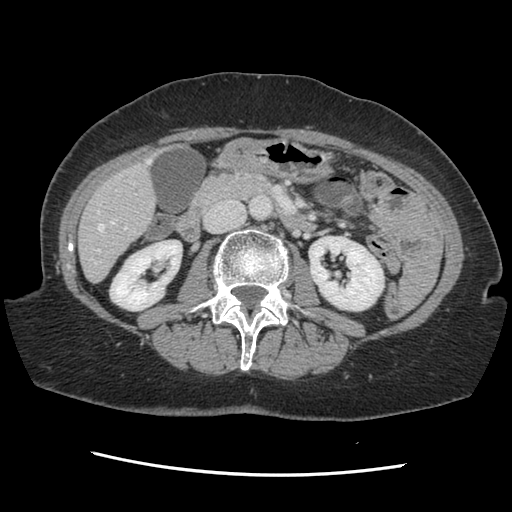
Contrast-enhanced abdominal CT, one axial slice; slice 50 of 141 in the series (ordered by position); soft-tissue window (W 400 / L 40 HU); 2.5 mm slice thickness; 512 × 512 image matrix, field of view 330 × 330 mm. Female patient, age 61 years. Case-level facts recorded for this patient, not image findings: diagnosis: colorectal cancer liver metastases, imaged before liver resection; multiple liver metastases: no; largest metastasis: 2.4 cm.
Outlined on this slice (manually delineated by an expert):
- hepatic veins: bounding box (x1, y1, x2, y2) in pixels: (95, 160, 151, 265)
- liver: (80, 158, 156, 281)
- planned liver remnant (the part of the liver to remain after resection): (80, 191, 155, 281)
- portal vein (with intrahepatic branches): (97, 227, 126, 252)